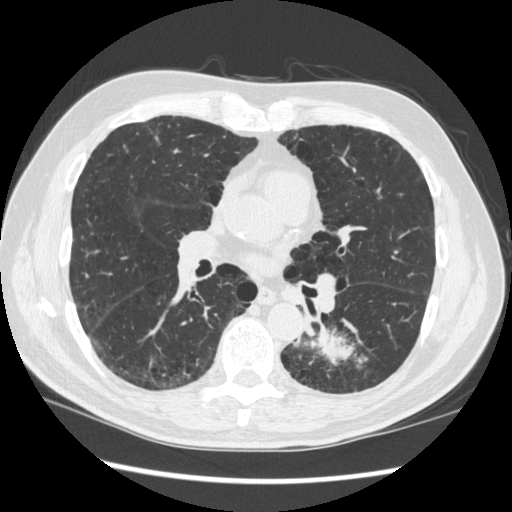
Low-dose screening chest CT, one axial slice. Position 167 of 348 along the scan axis. Reconstruction kernel STANDARD. 120 kVp. Lung window (W 1500 / L -600 HU). 1.25 mm slice thickness. 512 × 512 image matrix.
Structures marked on this image (outlined manually by an expert reader):
- lesion 1 (tumor, lower lobe of left lung): bounding box (x1, y1, x2, y2) in pixels: (306, 330, 366, 370)